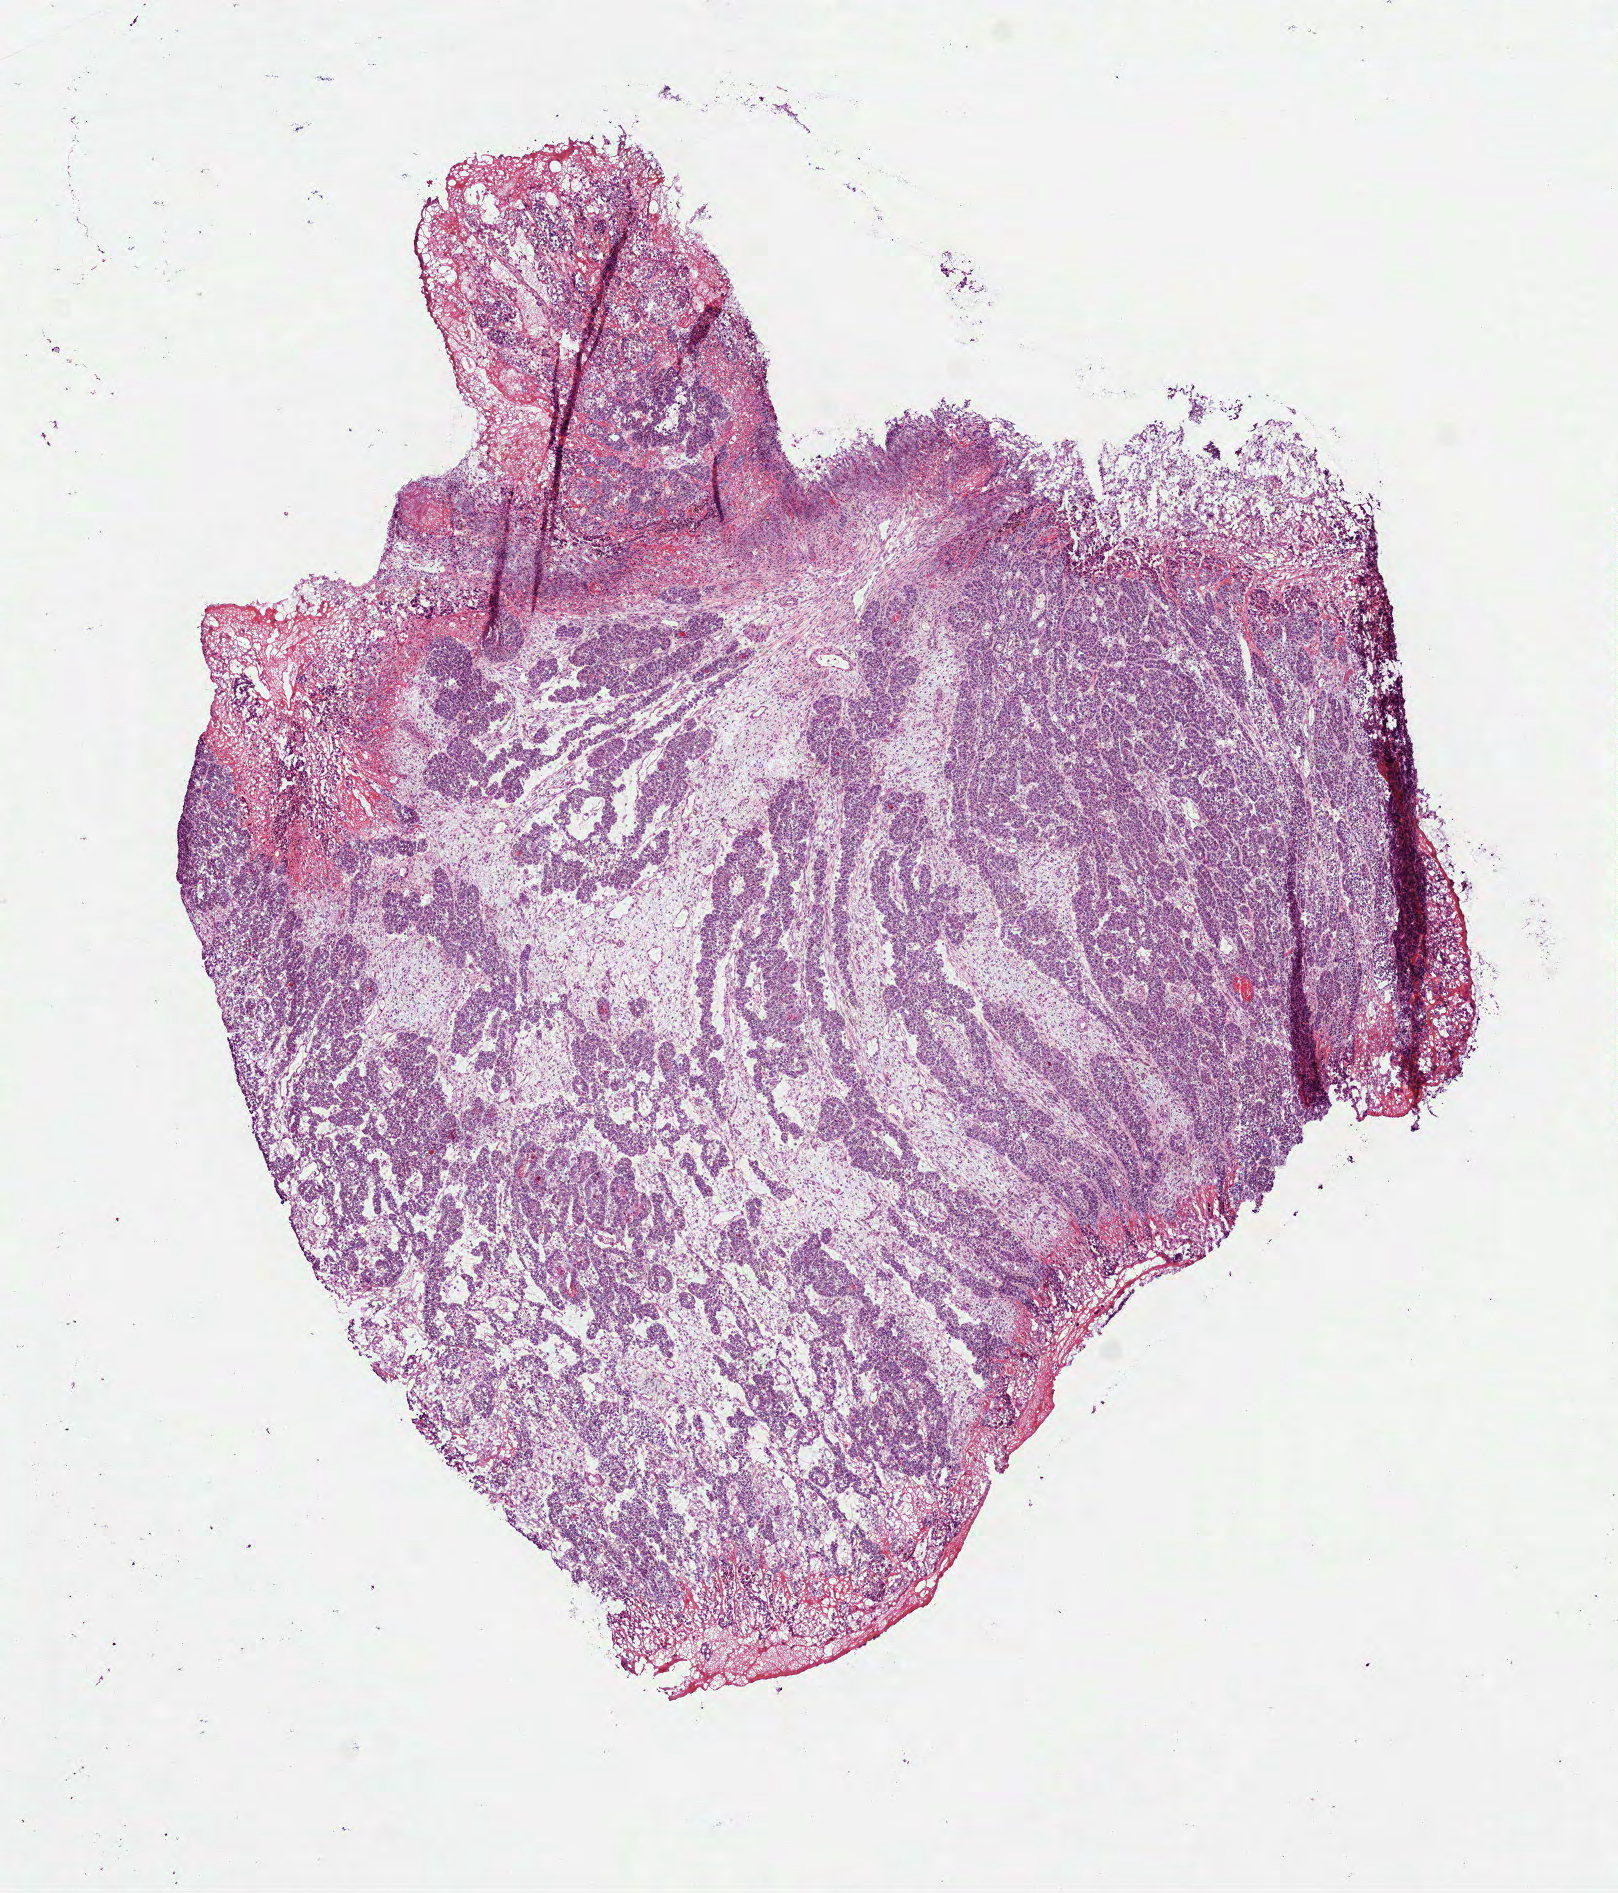
H&E-stained whole-slide image, low-resolution overview of the scanned area, about 6.5 x 7.6 mm, frozen section, primary tumour sample from the stomach. Patient: male, age at initial diagnosis 79 years. Histologic grade: G2 (moderately differentiated). Composition of this section per pathologist review: tumour cells 99%, tumour nuclei 85%, normal cells 0%, stromal cells 0%, necrosis 1%. Inflammatory infiltration, as recorded: lymphocyte infiltration 2%, monocyte infiltration 0%, neutrophil infiltration 0%.
Histologic diagnosis: Adenocarcinoma, NOS (gastric antrum). AJCC pathologic stage: IA (4th edition). Lymph nodes positive (case pathology): 0 of 17 examined.